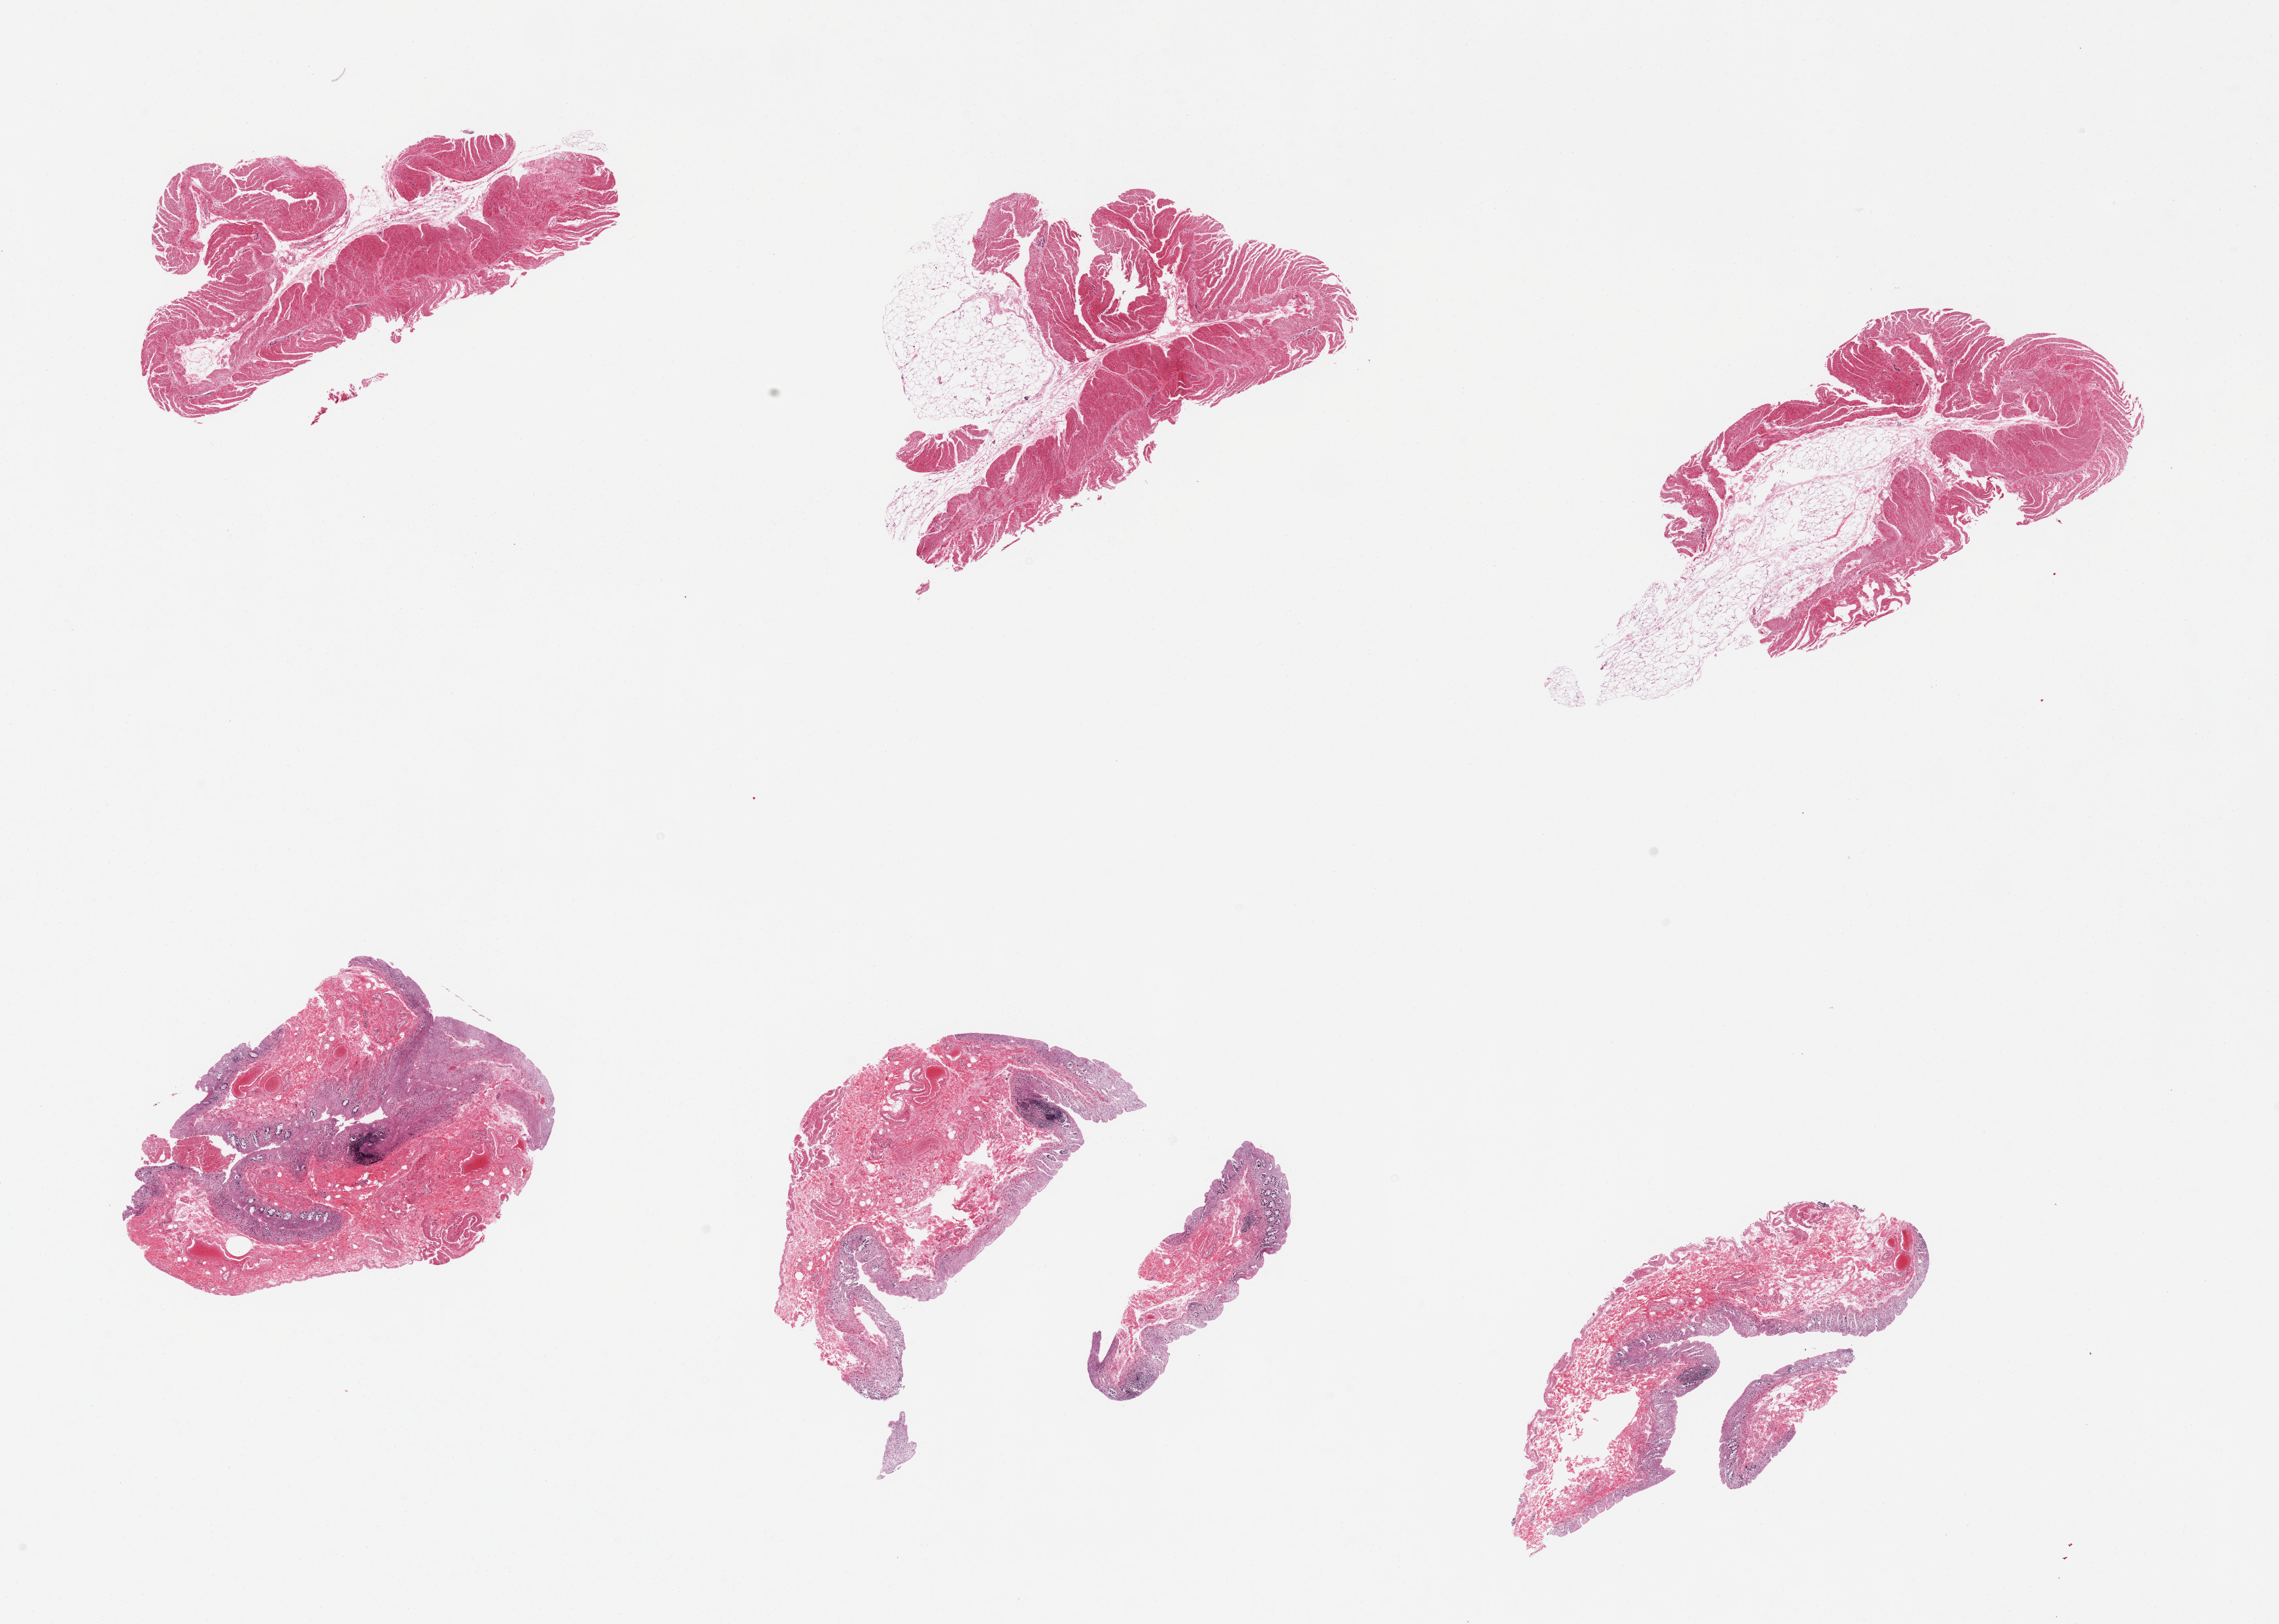
Haematoxylin and eosin whole-slide image, brightfield, low-resolution overview of the scanned area, about 27.6 x 19.6 mm, PAXgene-fixed paraffin-embedded (PFPE) section, sampled site (target tissue): transverse colon, tissue donor sample. Donor sex: male.
• reviewer comment on this tissue sample: 7 pieces with variable combination of severely autolyzed mucosa and muscularis